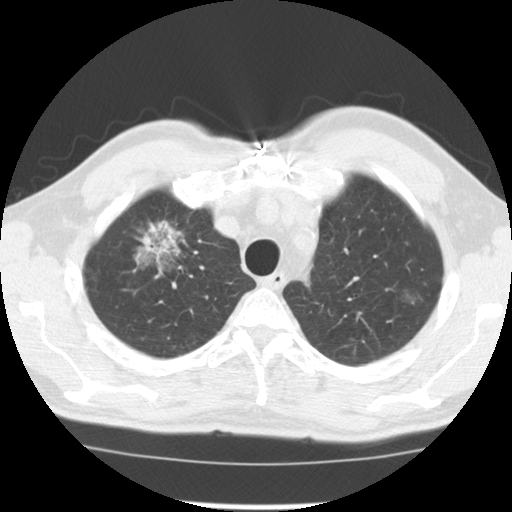
Axial slice from a low-dose chest CT screening exam, third annual screen, lung window (W 1500 / L -600 HU), 2.5 mm slice thickness, standard (soft-tissue) reconstruction kernel (STANDARD), 120 kVp, slice 26 of 128 in the series, 512 × 512 image matrix, field of view 340 × 340 mm. Male, age 64 years at enrolment. Former smoker at enrolment.
• Lesion marked by an expert reader, bounding box (x1, y1, x2, y2) in pixels: (126, 224, 201, 287).
• The screening reader recorded 3 non-calcified nodules or masses ≥4 mm on this exam (right upper lobe, right lower lobe, left upper lobe); which of them this box marks is not recorded.
• Lung cancer was diagnosed 30 days after this screen: adenocarcinoma, NOS, right upper lobe, well differentiated (G1), stage IB (AJCC 6th edition), 45 mm at pathology.